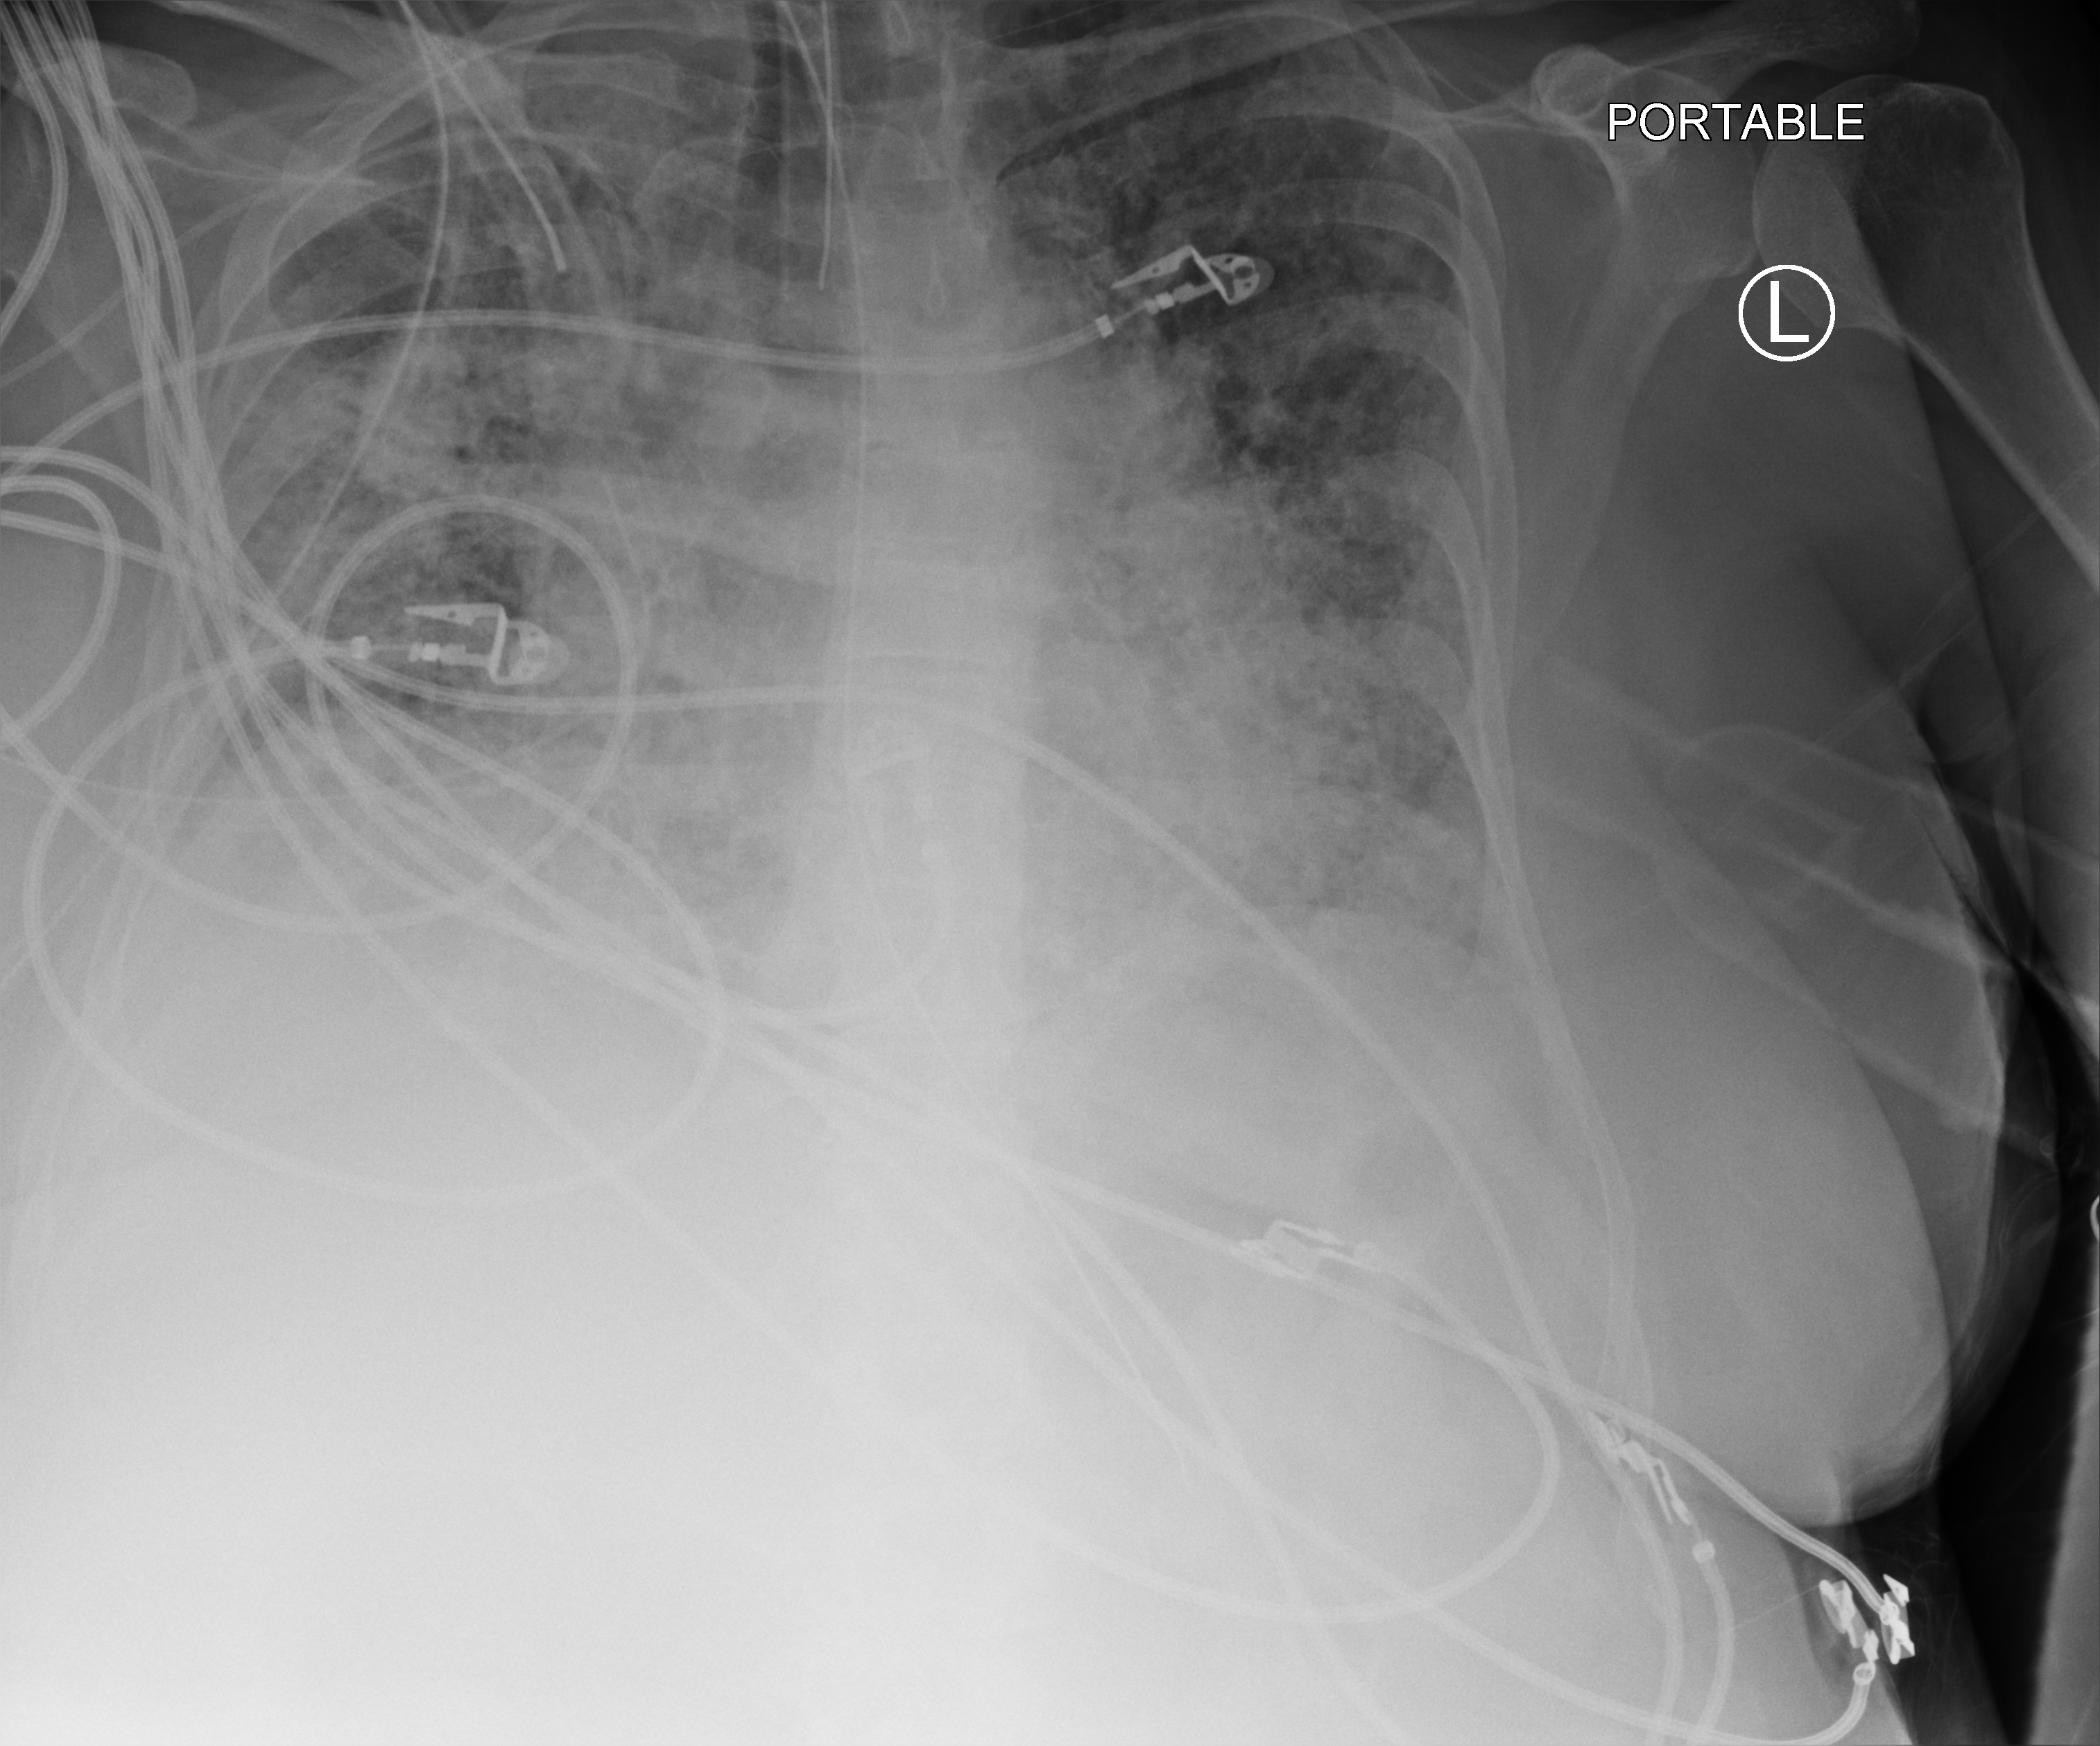
Bedside chest radiograph (computed radiography), anteroposterior (AP) projection. Patient hospitalised with COVID-19; female, aged 60–74 years.
From the hospital-stay record, not from the radiograph (when in the stay this image was taken is not recorded):
- length of hospital stay: 45 days